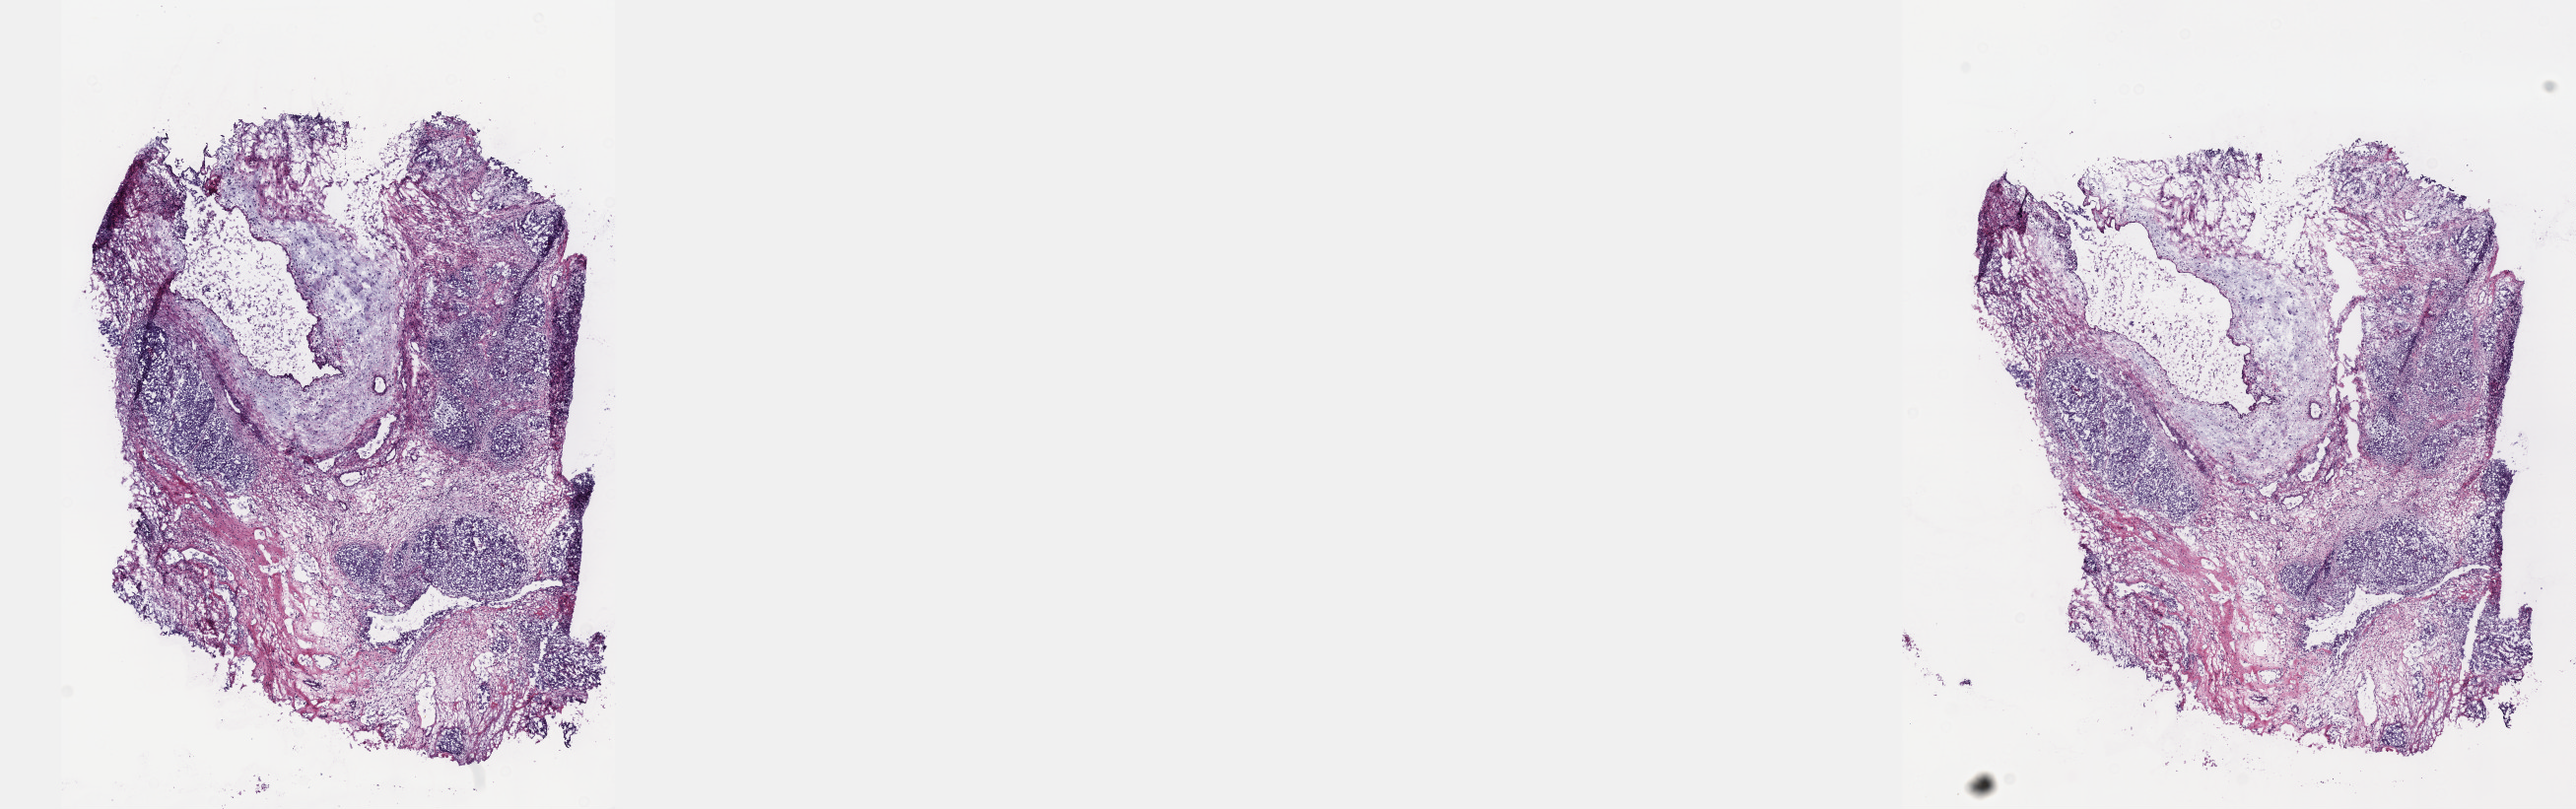
Whole-slide histology image, Hematoxylin and eosin (H&E) stained — shown as a low-resolution overview of the whole scanned area (about 21.1 x 6.6 mm), frozen section from the top of the tissue portion, primary tumour sample from the testis. Patient: male, age at initial diagnosis 23 years. Composition of this section per pathologist review: tumour cells 95%, tumour nuclei 85%, normal cells 0%, stromal cells 0%, necrosis 5%. Infiltration values recorded for this section: lymphocyte infiltration 0%, monocyte infiltration 0%, neutrophil infiltration 0%.
- diagnosis: Embryonal carcinoma, NOS
- laterality: left
- AJCC pathologic stage: IIIC (7th edition)